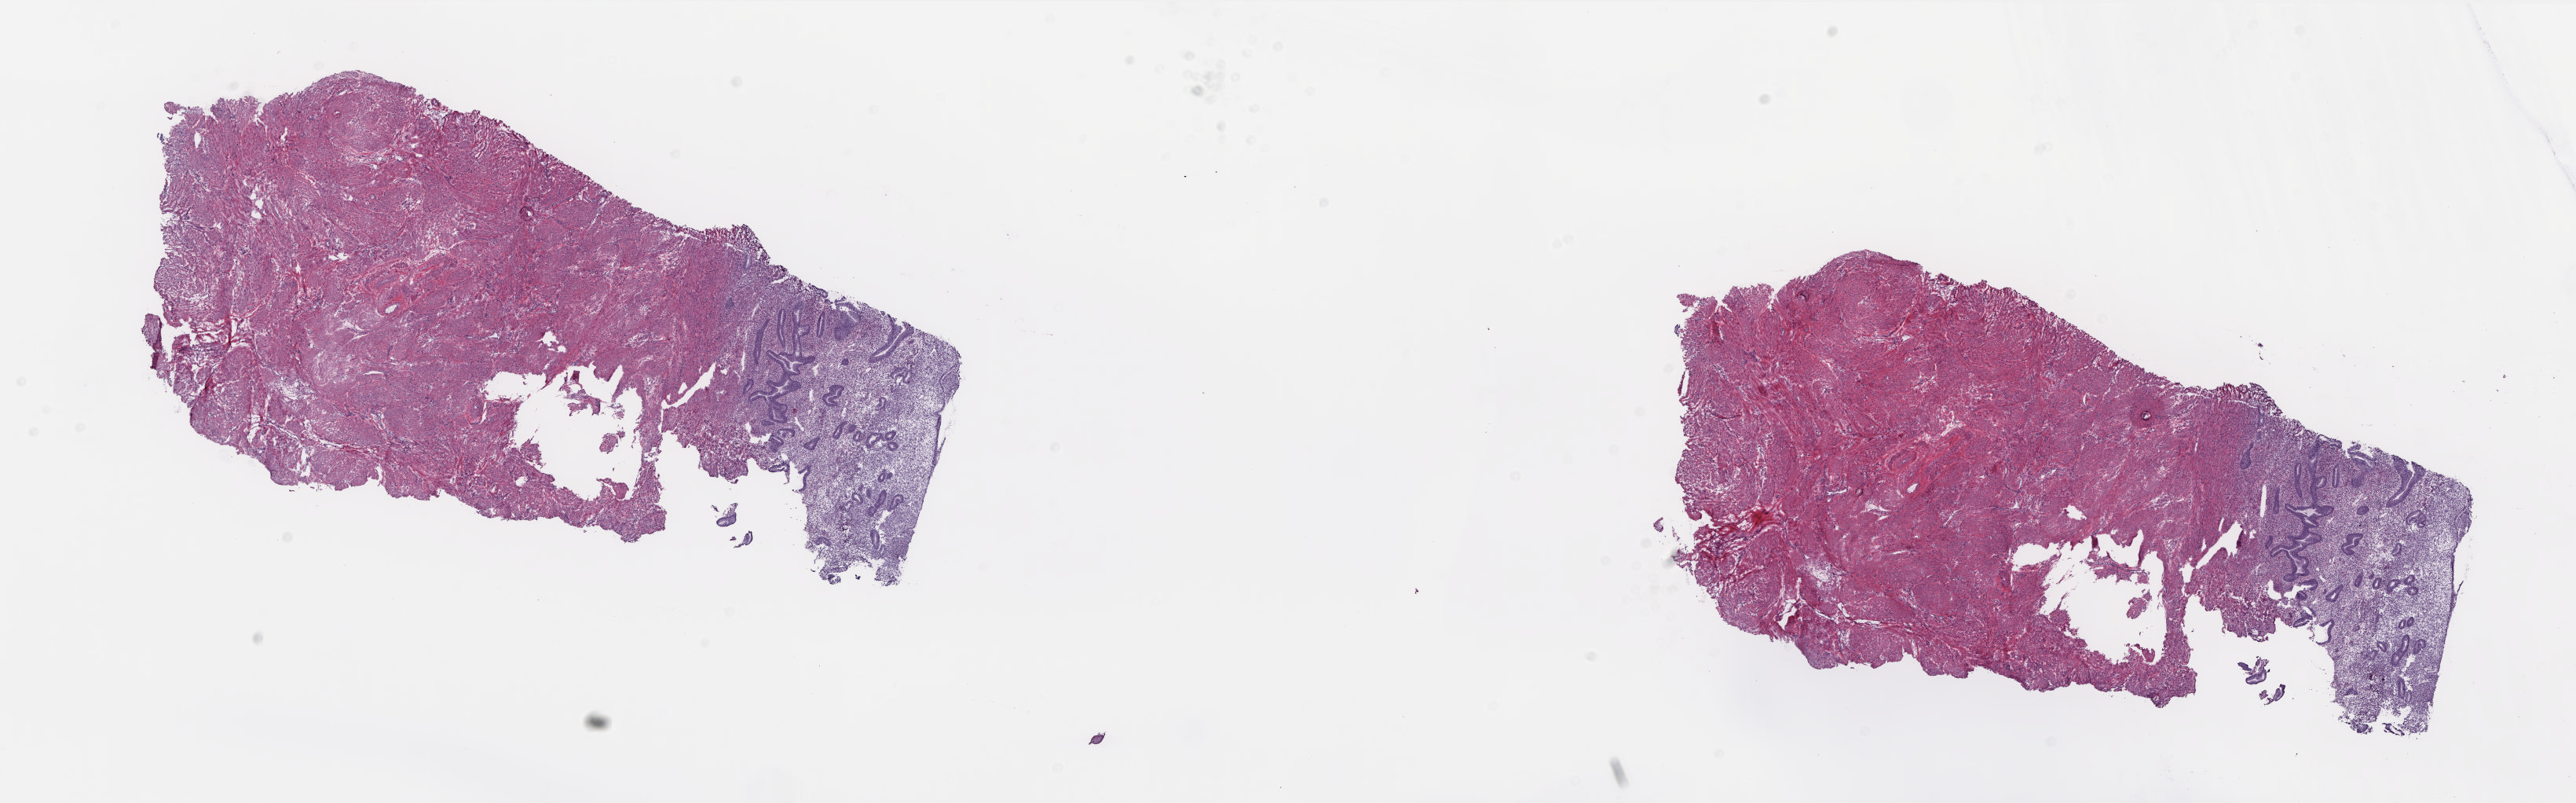
H&E-stained whole-slide image — a low-resolution overview of the entire scanned area, about 26.5 x 8.2 mm (acquisition: 20x scan), frozen section, sample: solid tissue normal (non-tumour tissue), uterus. Patient: female, age at initial diagnosis 42 years. Slide review estimates, as recorded: tumour cells 0%, tumour nuclei 0%.
This section: solid tissue normal (non-tumour) sample from the same patient. Patient diagnosis: Endometrioid adenocarcinoma, NOS (endometrium).